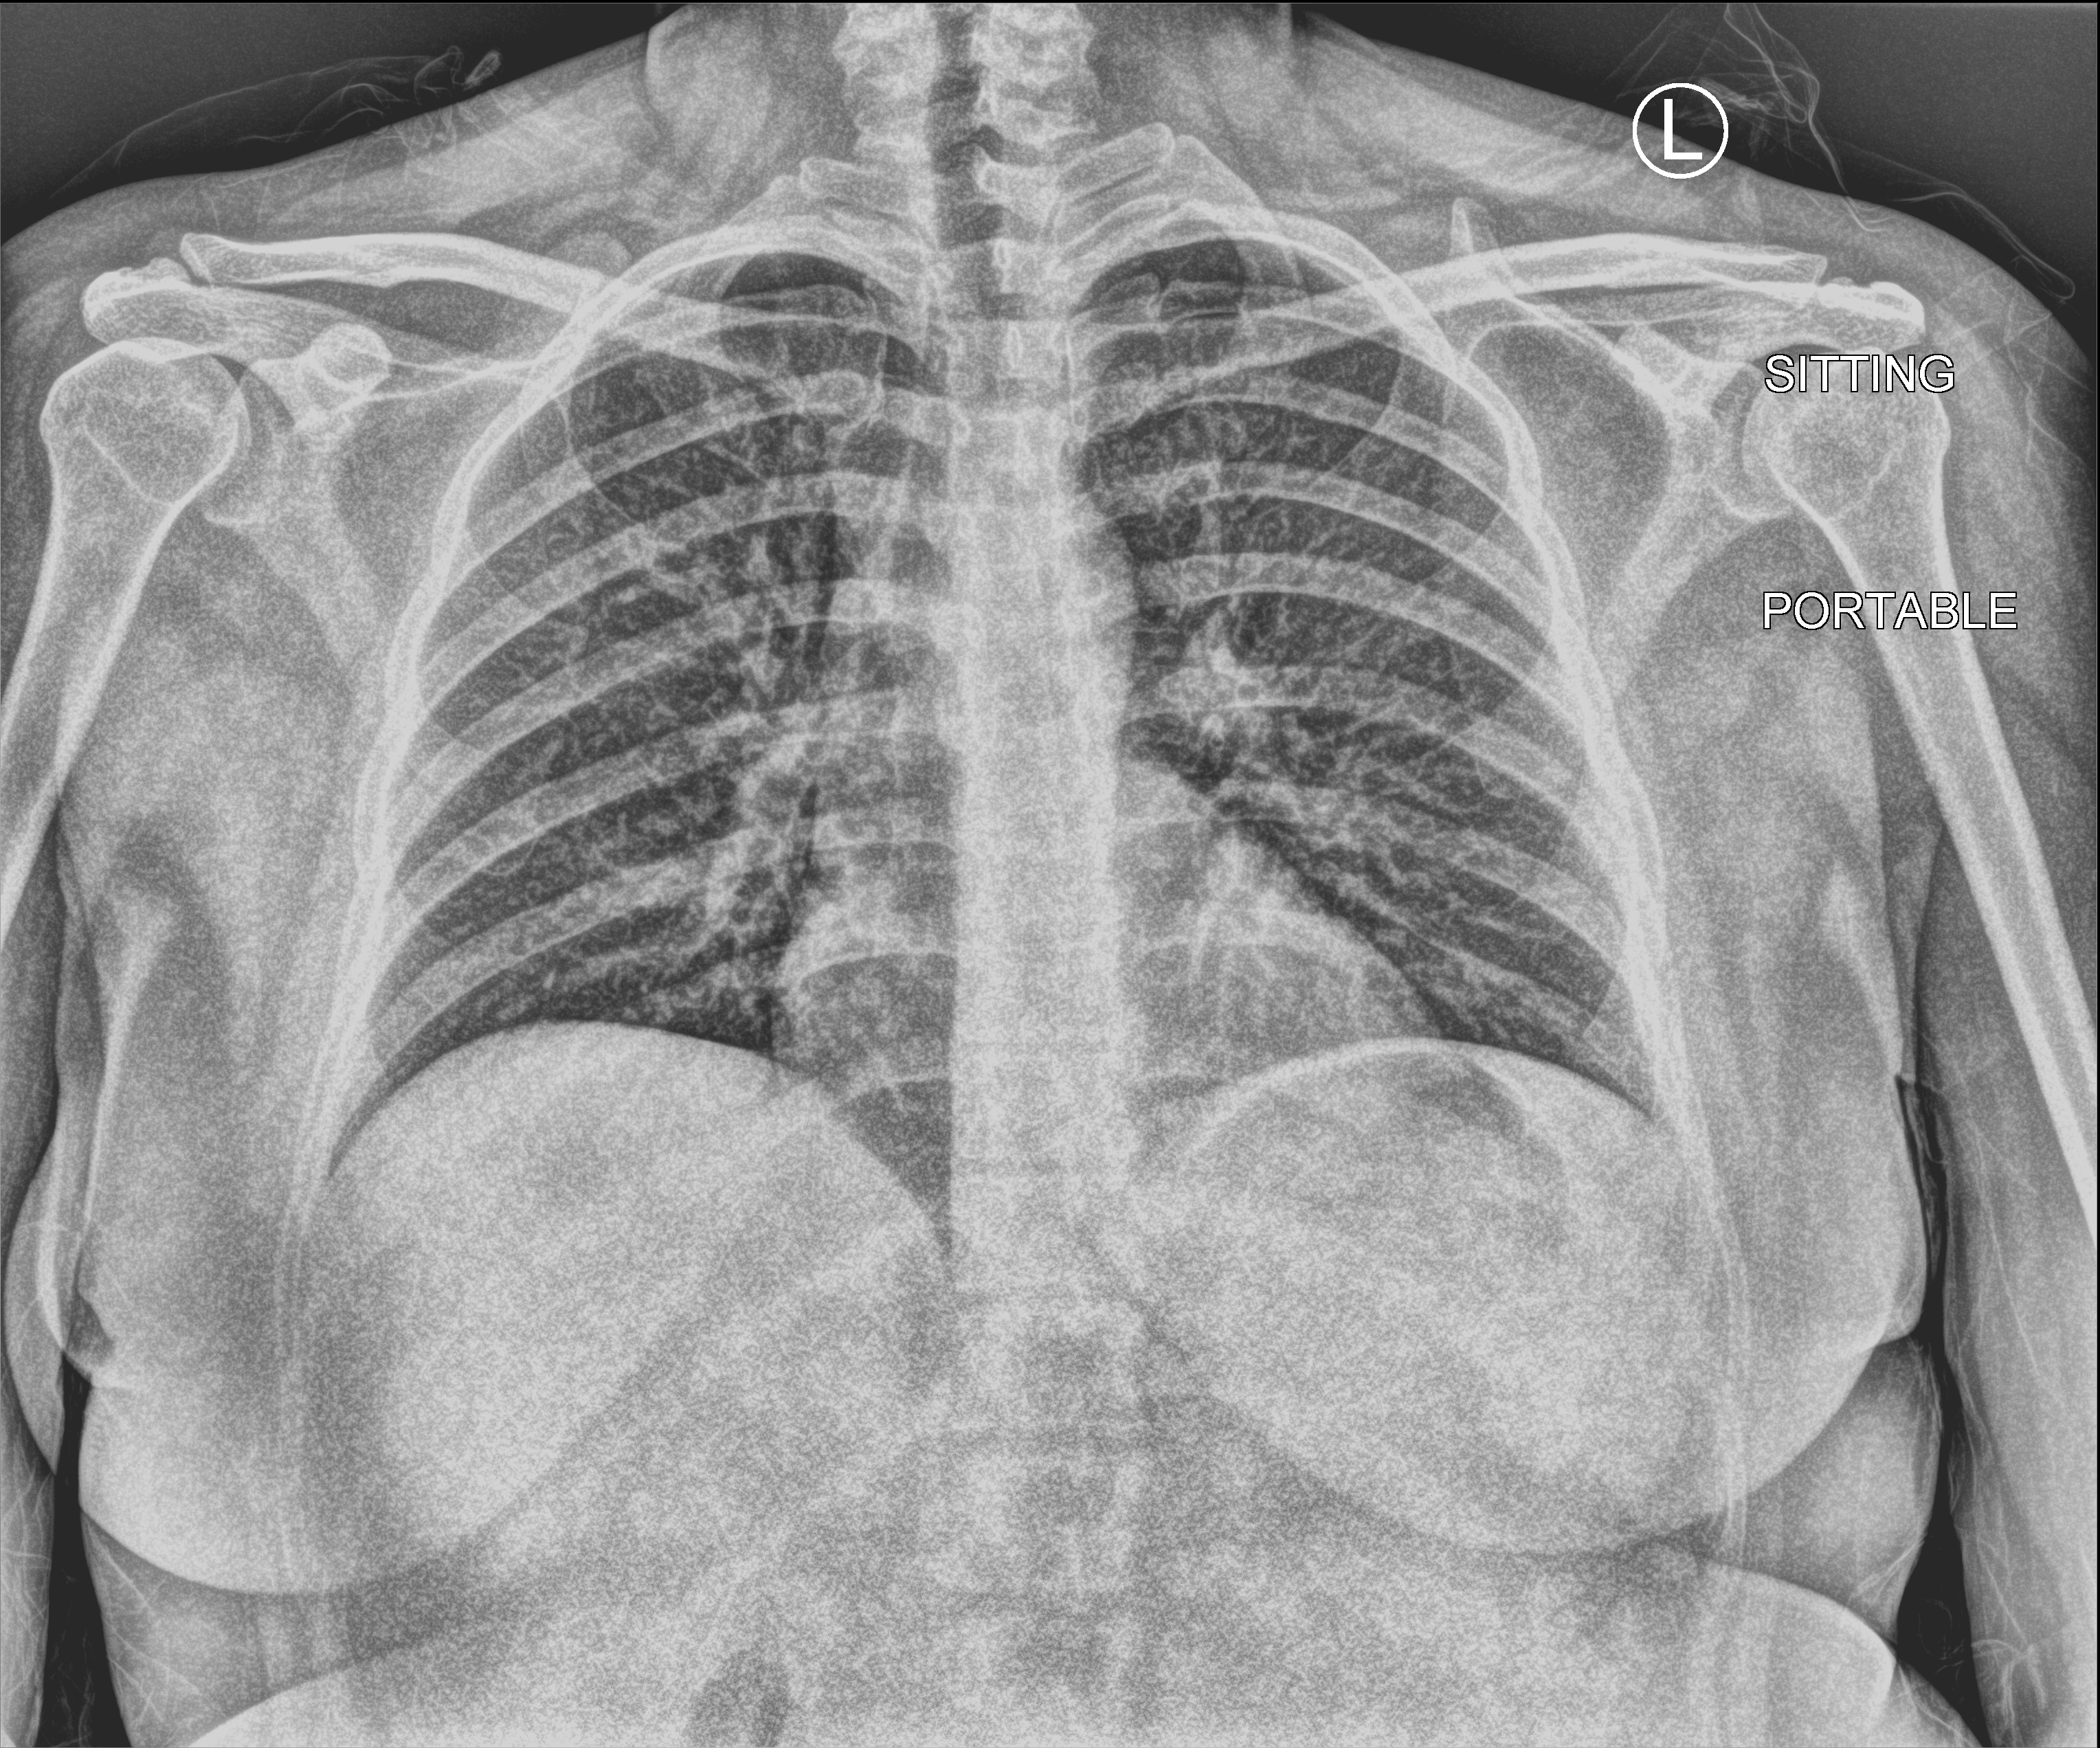
Bedside chest radiograph (computed radiography); anteroposterior (AP) projection. Female patient hospitalised with COVID-19, age 18–59 years.
Hospital-stay facts (about this admission, not read from this image; timing relative to this image not recorded):
- mechanically ventilated during this hospital stay: no
- admitted to intensive care during this hospital stay: no